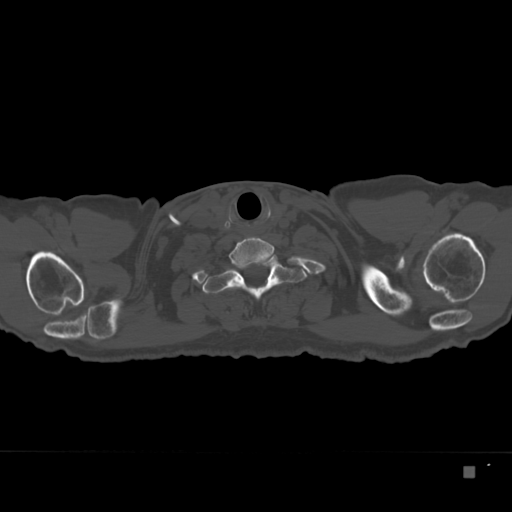
CT including the spine, one axial slice; slice 320 of 332 in the series (ordered by position); bone window (W 1800 / L 400 HU); 1.5 mm slice thickness; 512 × 512 image matrix, field of view 389 × 389 mm. Male patient, age 72 years. Case-level facts recorded for this patient, not image findings: primary cancer: skeletal.
Annotated regions visible in this slice (semi-automatic segmentation, software-assisted and operator-edited):
- T1 vertebra: bounding box (x1, y1, x2, y2) in pixels: (202, 254, 307, 300)